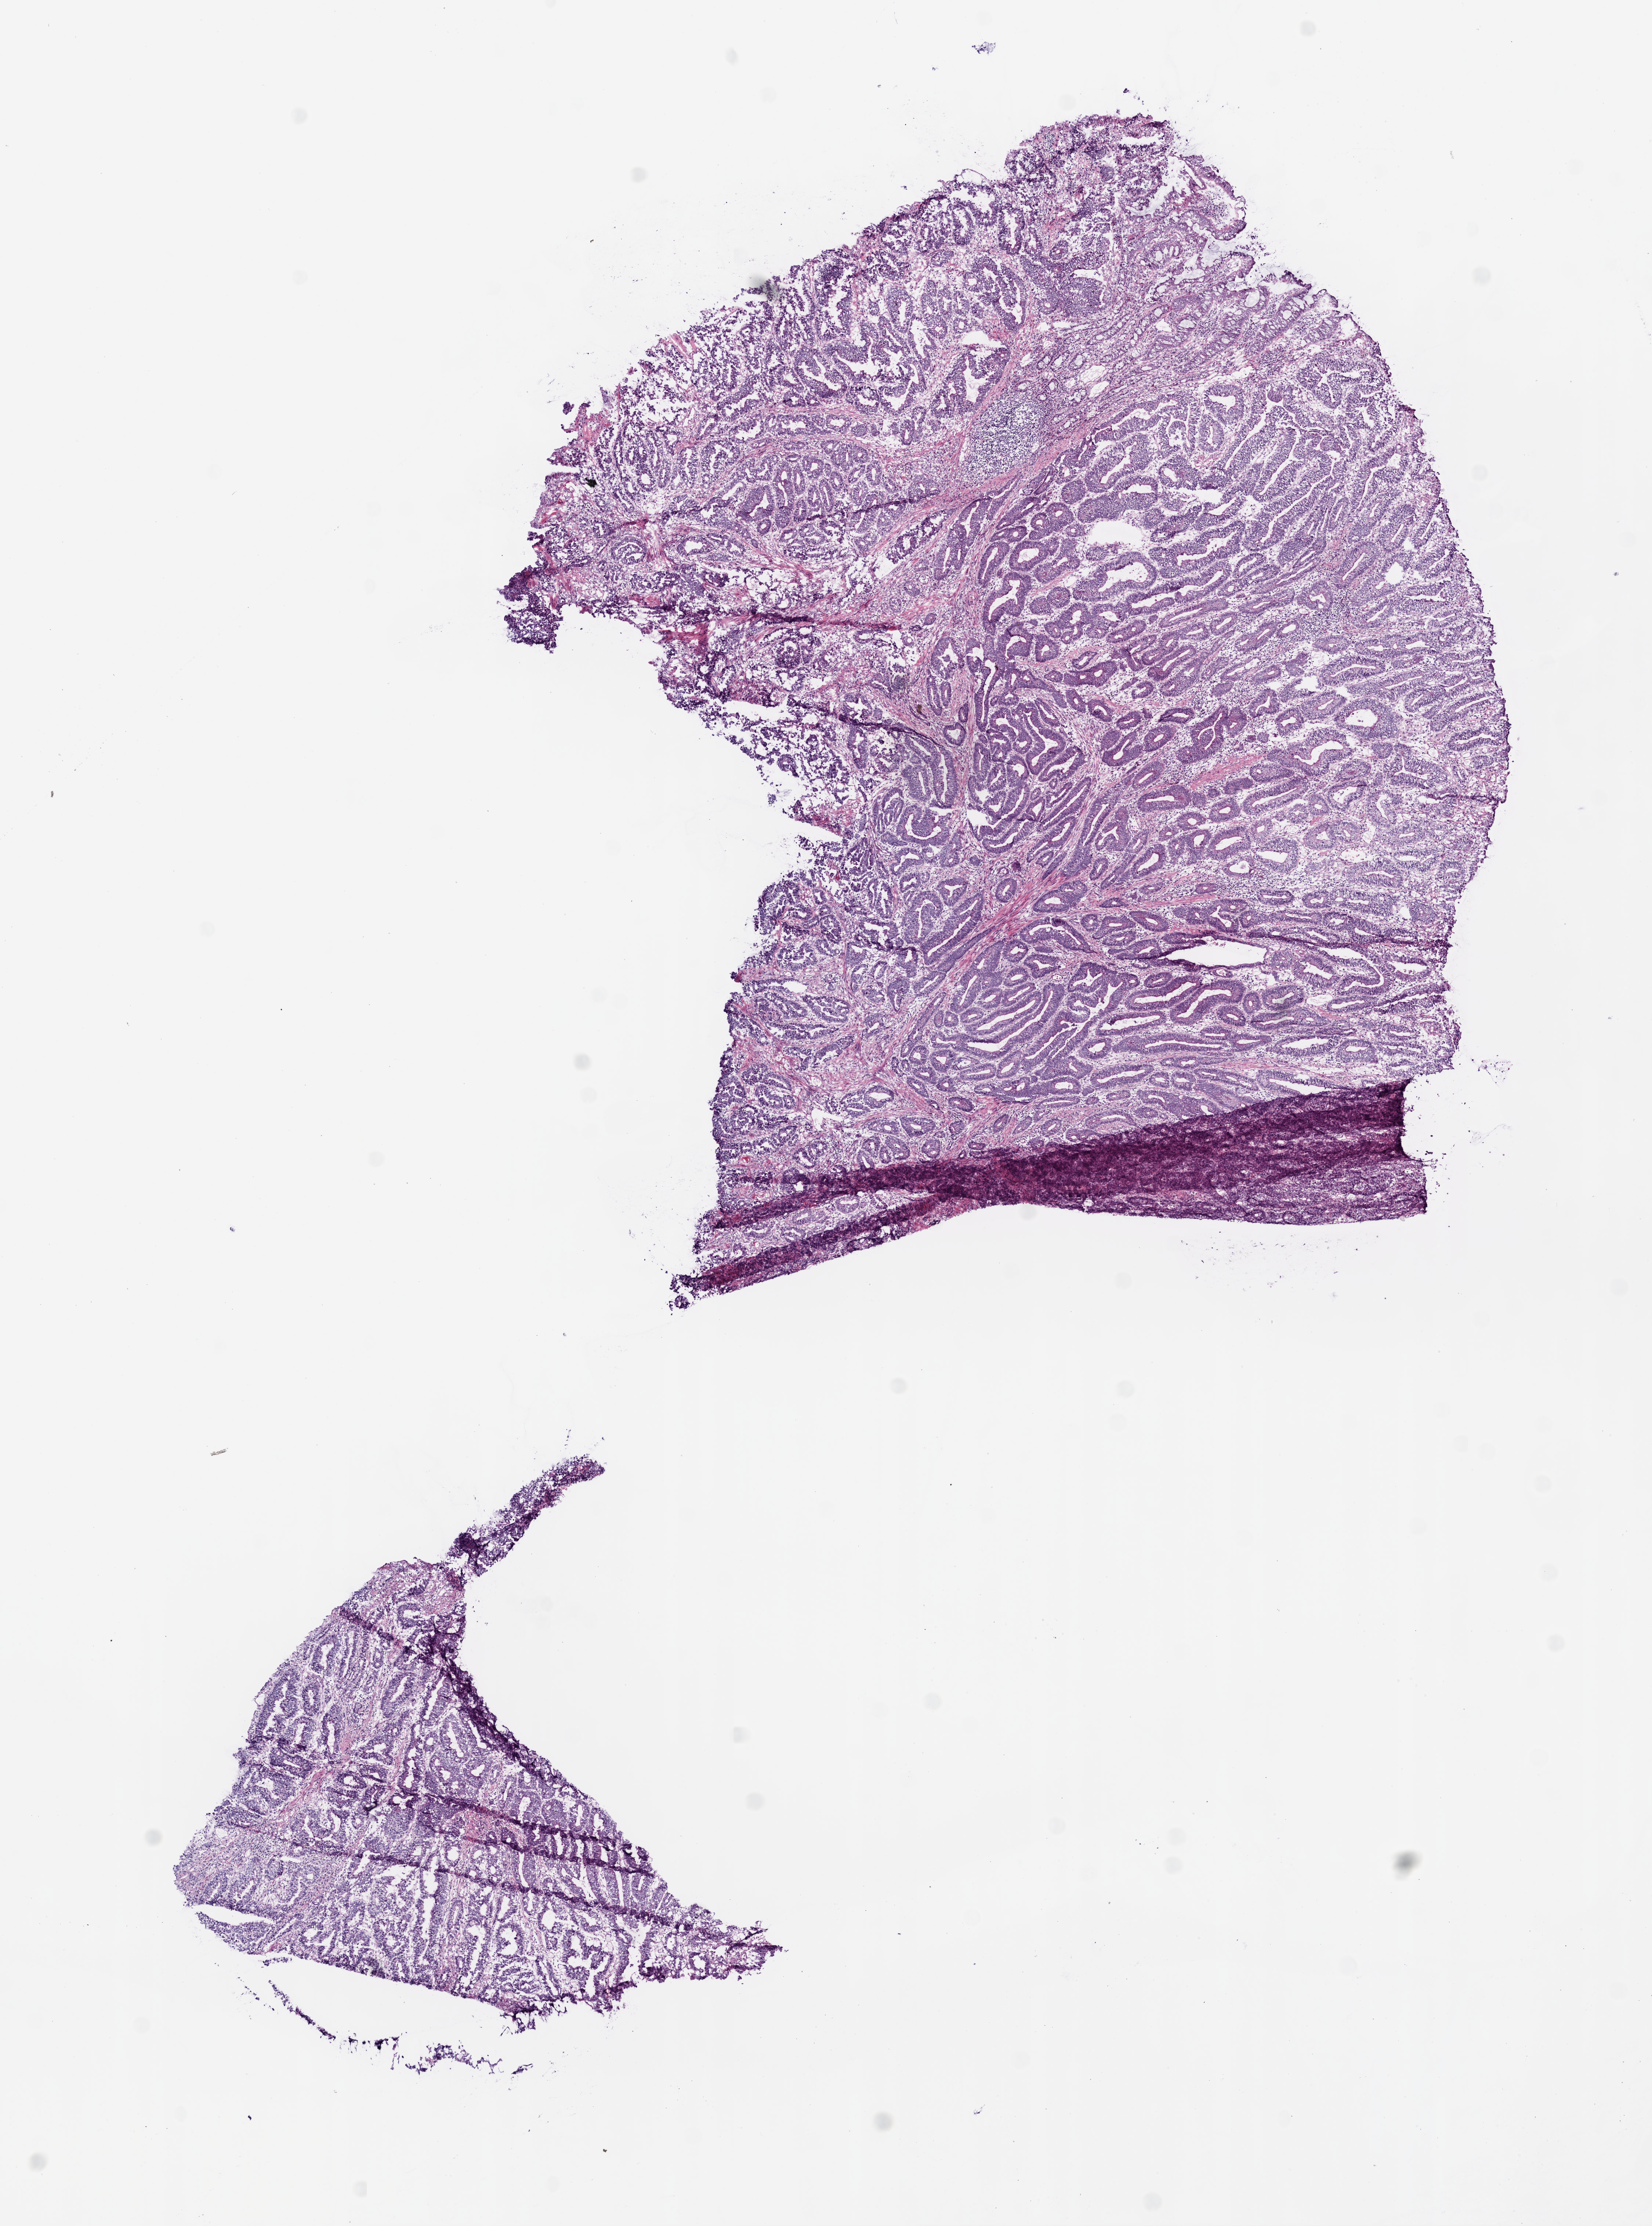
Whole-slide histology image, Hematoxylin and eosin (H&E) stained — a low-resolution overview of the entire scanned area, about 9.0 x 12.2 mm, frozen section from the bottom of the tissue portion, sample: primary tumour, rectum. Patient: male, age at initial diagnosis 68 years. Pathologist review of this section (percent, as recorded): tumour cells 85%, tumour nuclei 75%, normal cells 0%, stromal cells 10%, necrosis 5%.
Lymph nodes positive (case pathology): 0 of 32 examined. AJCC pathologic stage: IIA (6th edition). Pathologic diagnosis: Adenocarcinoma, NOS (rectosigmoid junction).